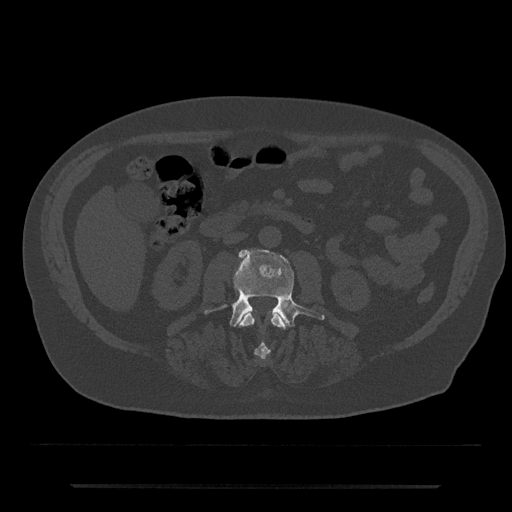
CT including the spine, one axial slice. Position 429 of 797 along the scan axis. Reconstruction kernel Br40s/3. 120 kVp. Bone window (W 1800 / L 400 HU). 0.5 mm slice thickness. 512 × 512 image matrix. Patient: male, 80 years. From the clinical record (not read from this slice): primary cancer: prostate.
Outlined on this slice (semi-automatically segmented with operator editing):
- L2 vertebra: bounding box <239,311,285,360> (left, top, right, bottom; pixels)
- L3 vertebra: <204,249,325,328>